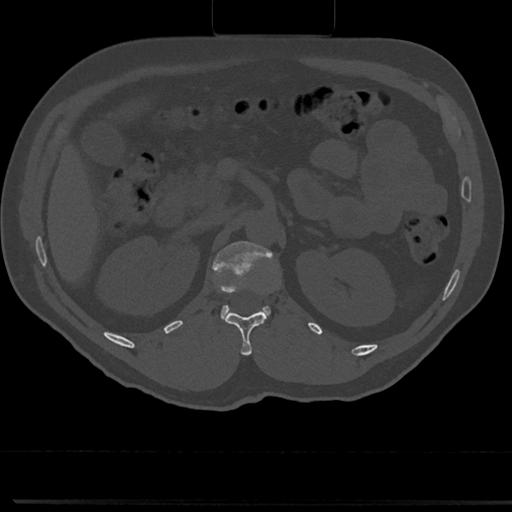
CT including the spine, one axial slice; slice 115 of 817 in the series (ordered by position); reconstruction kernel Br40s/3; bone window (W 1800 / L 400 HU); 512 × 512 image matrix, field of view 355 × 355 mm. Patient: male, 61 years. Case-level facts recorded for this patient, not image findings: primary cancer: prostate.
Outlined on this slice (semi-automatically segmented with operator editing):
- L1 vertebra: bounding box [x1, y1, x2, y2] px = [212, 240, 278, 325]
- T12 vertebra: [223, 310, 268, 355]